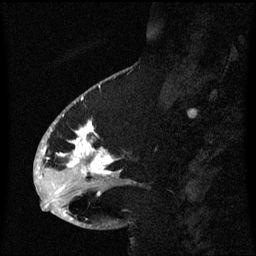
Breast MRI (dynamic contrast-enhanced), one sagittal slice. Slice 25 of 60 in the series (ordered by position). Dynamic contrast-enhanced series, image 2 of 3 at this slice position (ordered by acquisition). 1.5 T. TE 4.2 ms, TR 8.4 ms. 256 × 256 image matrix, field of view 200 × 200 mm. Female patient, age 53 years. From the clinical record (not read from this slice): setting: breast cancer imaged before/during neoadjuvant chemotherapy; receptor status: HR-positive, HER2-negative.
Annotated regions visible in this slice (semi-automatic segmentation, software-assisted and operator-edited):
- analysis volume of interest (the breast-tissue region the enhancement analysis was run in; not a lesion): box from (x=49, y=108) to (x=132, y=201) px
- tumour enhancement mask (voxels above the 70 % enhancement threshold inside the analysis volume of interest): (x=61, y=122)–(x=115, y=175)